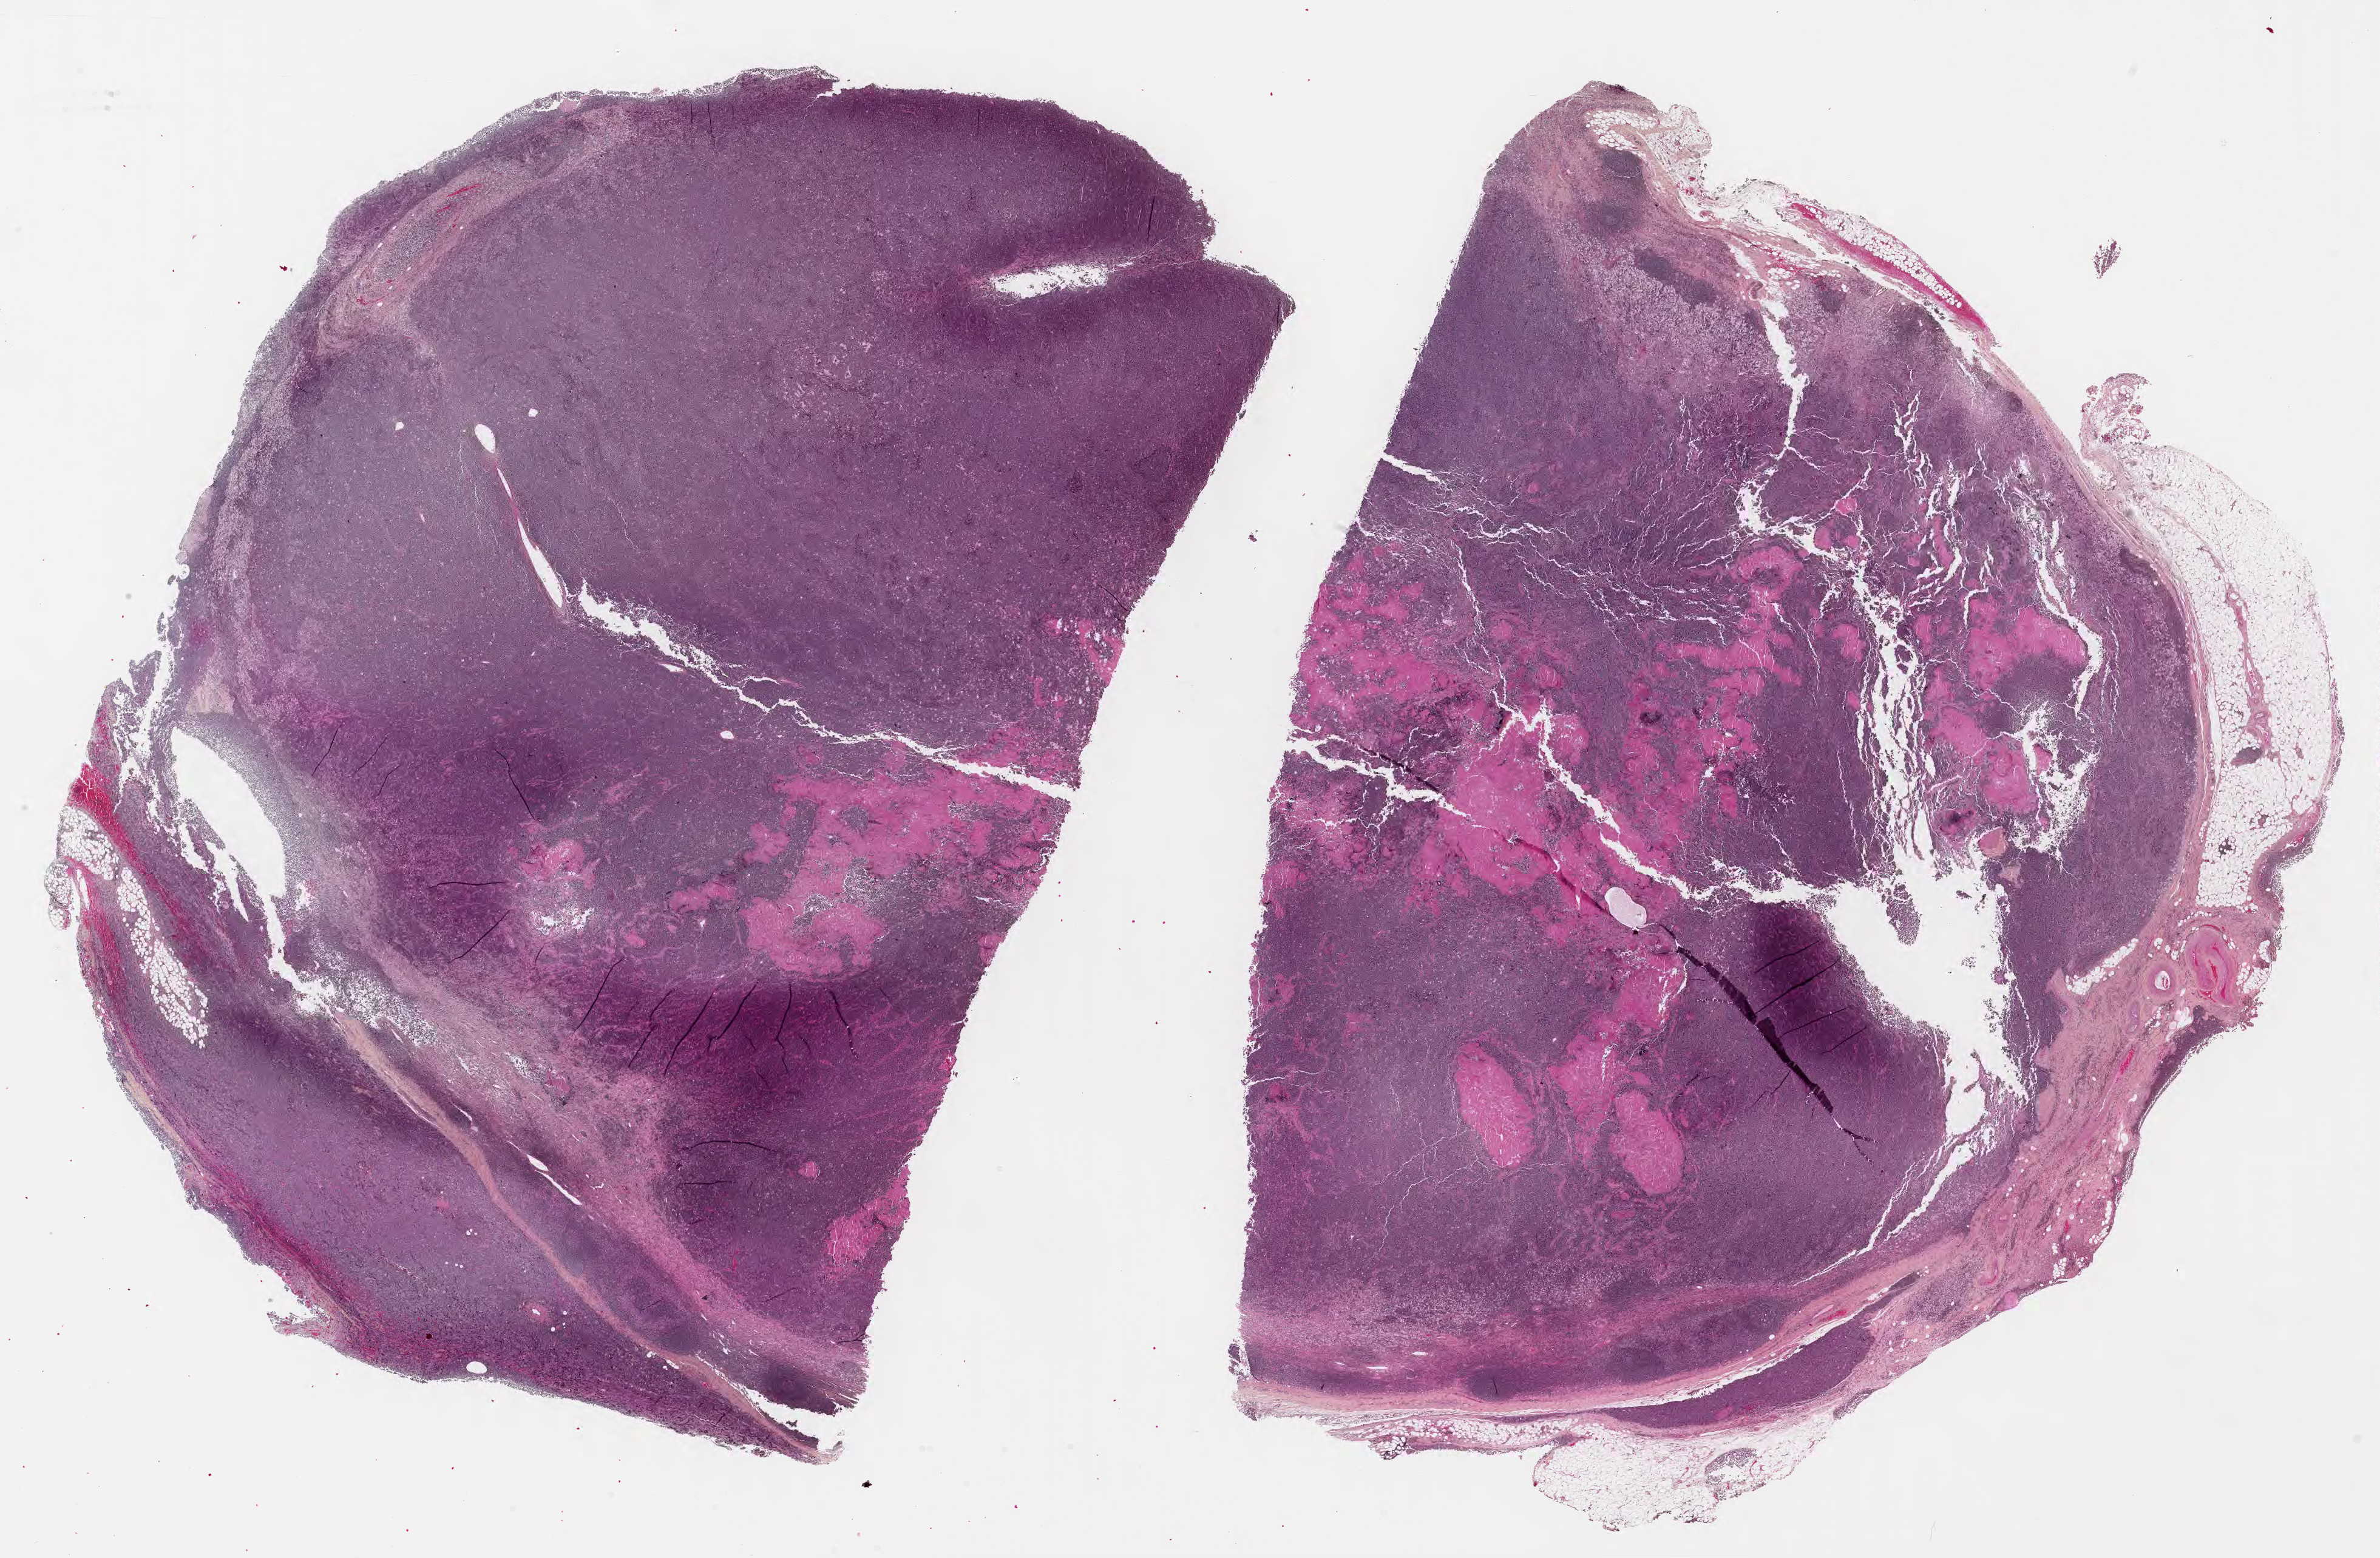
Whole-slide image, hematoxylin and eosin (H&E) stain — low-resolution overview of the scanned area, about 31.7 x 20.7 mm. Formalin-fixed paraffin-embedded section. Specimen: primary tumor. Male patient, age 48 years. Composition of this section per pathologist review: tumor cells 85%, tumor nuclei 90%, stromal cells 10%, necrosis 5%, normal cells 0%. Inflammatory infiltration, as recorded: lymphocyte infiltration 10%, monocyte infiltration 30%, neutrophil infiltration 10%.
Ann Arbor stage (patient): Stage IV. Section: top of the tissue portion. Histologic diagnosis: Burkitt lymphoma, NOS.